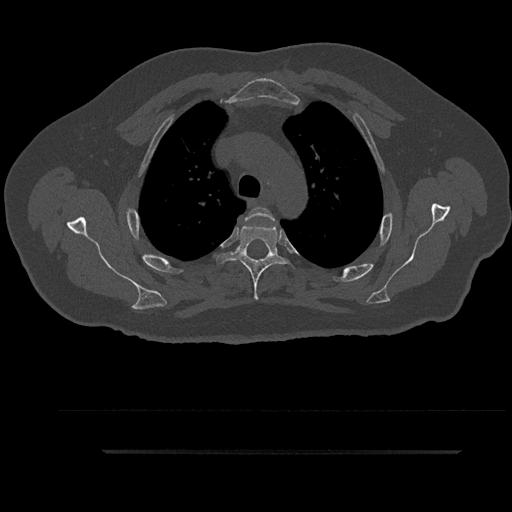
CT including the spine, one axial slice; position 678 of 797 along the scan axis; bone window (W 1800 / L 400 HU); 0.5 mm slice thickness; 512 × 512 image matrix, field of view 432 × 432 mm. Patient: male, 63 years. From the clinical record (not read from this slice): primary cancer: renal.
Outlined on this slice (semi-automatically segmented with operator editing):
- T3 vertebra: bounding box [x1, y1, x2, y2] px = [245, 207, 275, 259]
- T4 vertebra: [216, 224, 288, 301]